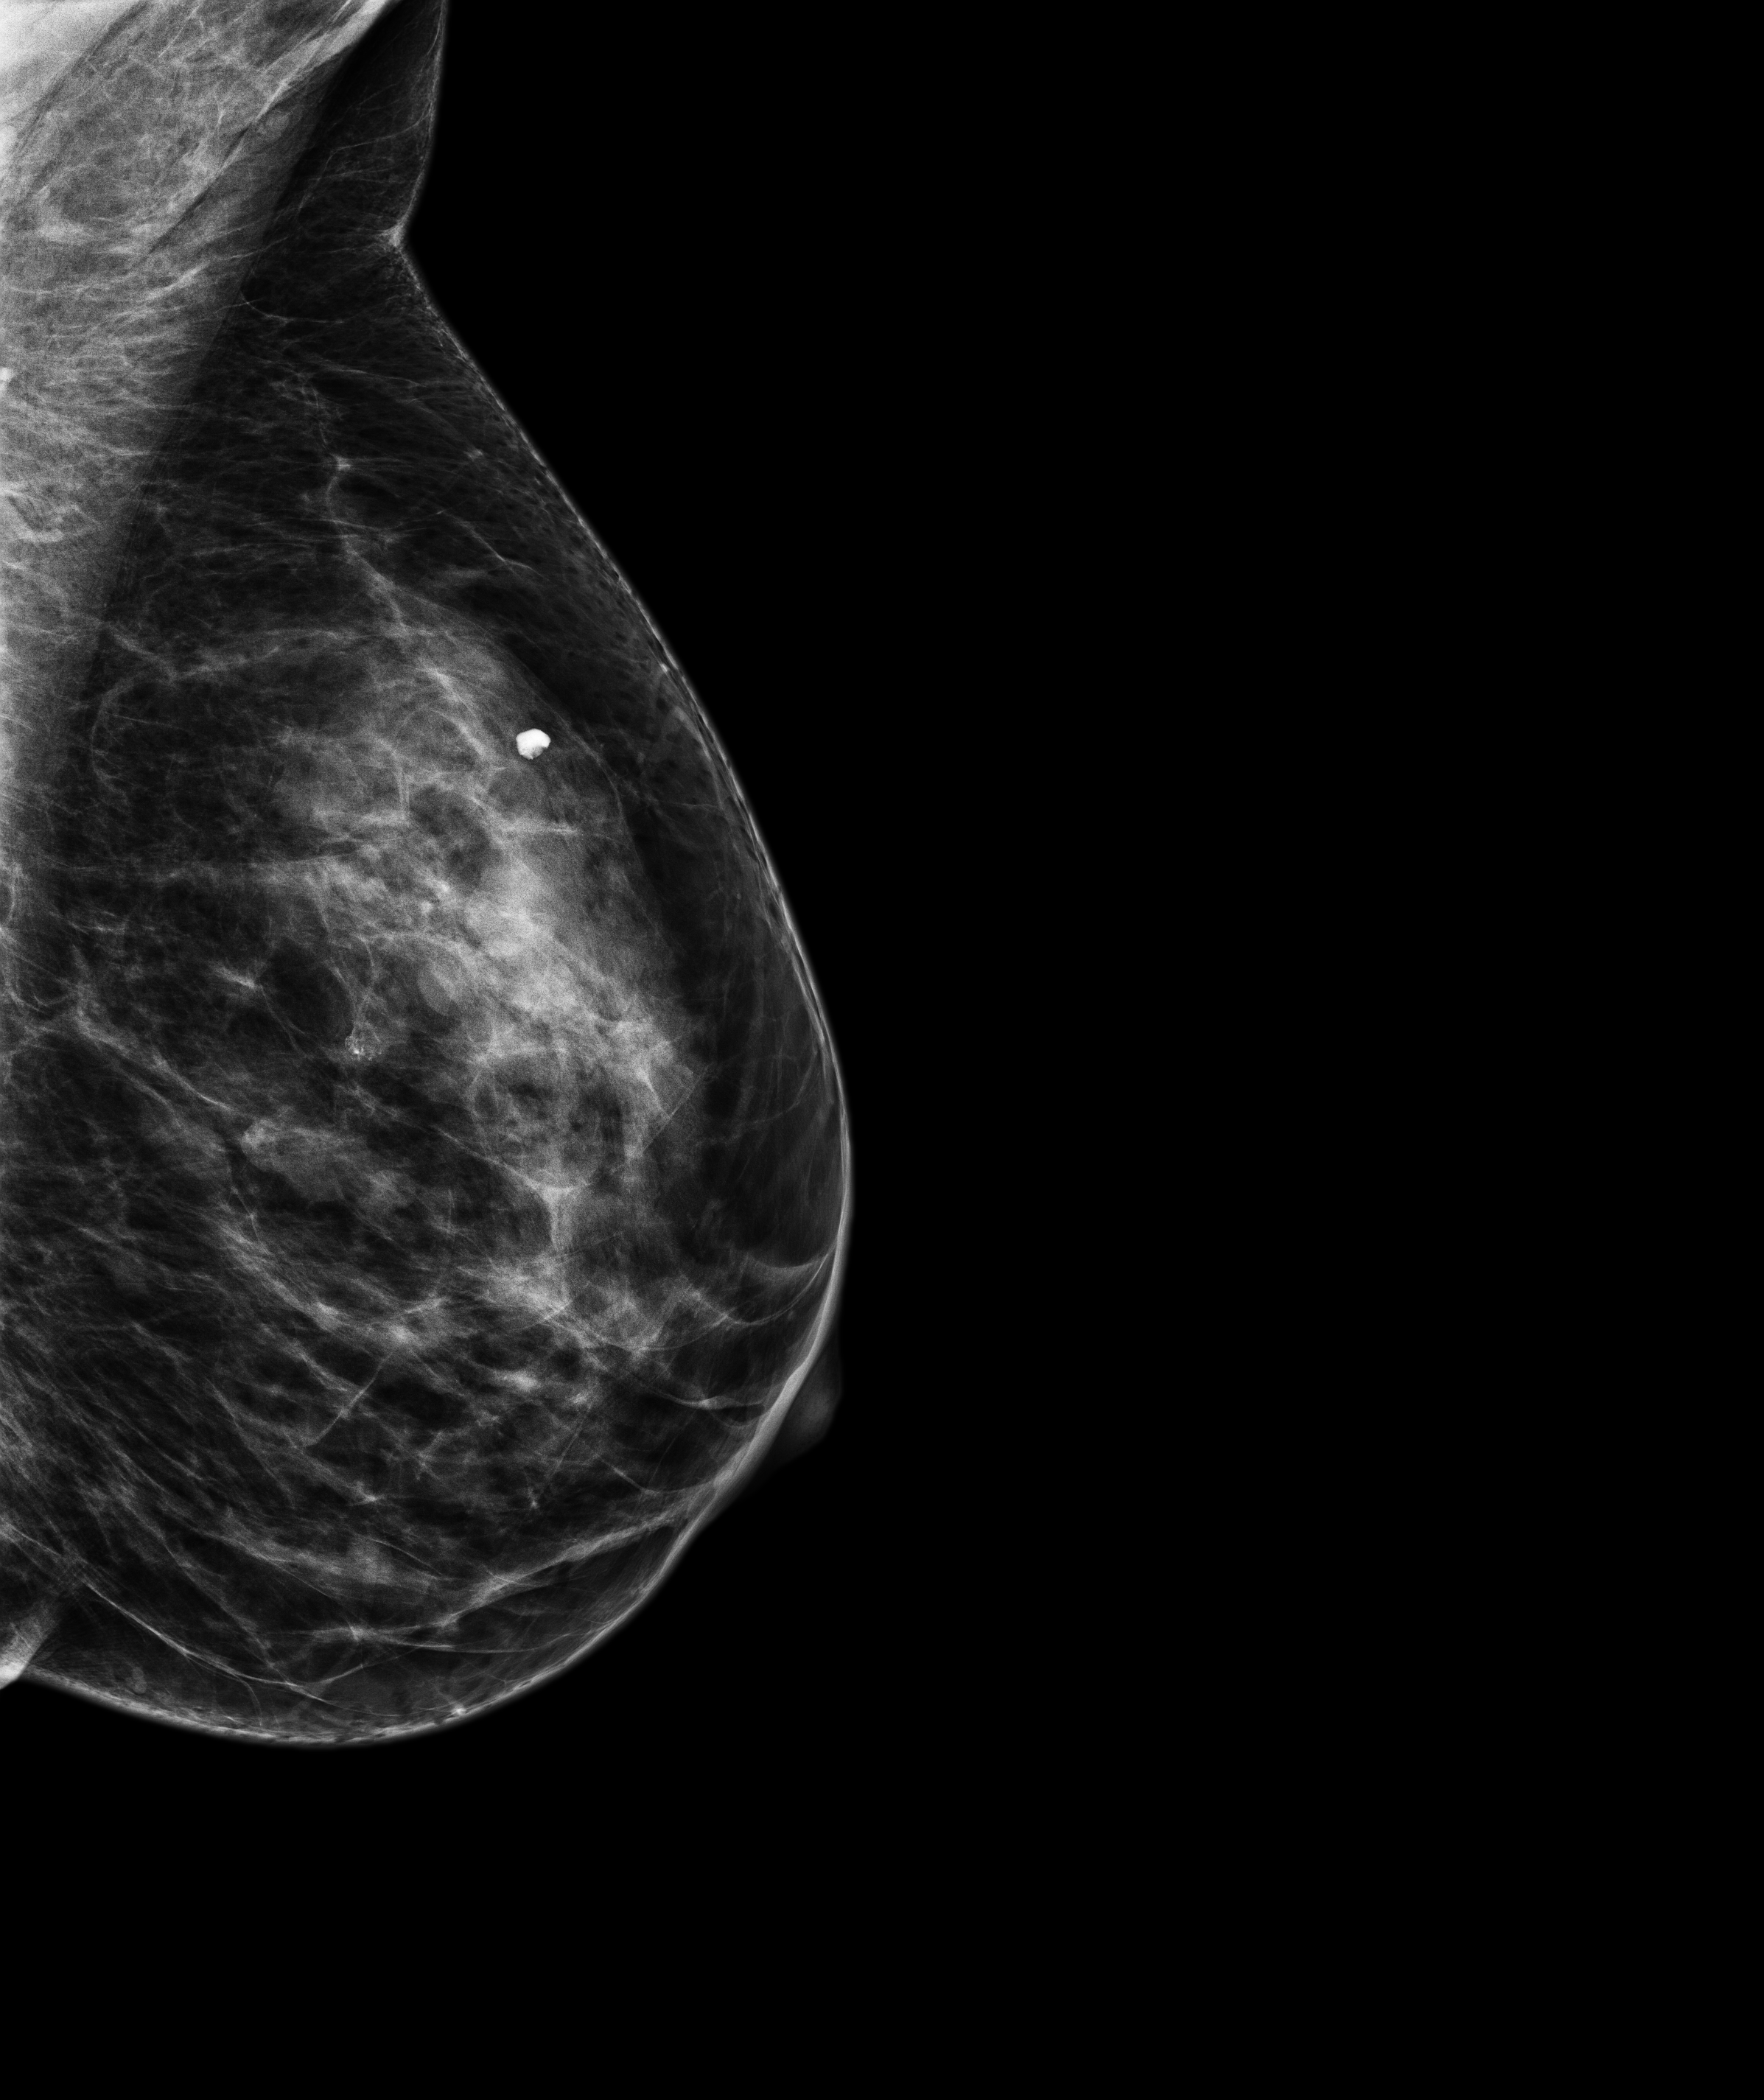
Screening examination, compressed breast thickness 60.3 mm. Patient aged 52 years (female).
Image type: full-field digital mammogram. Breast: left. Projection: medio-lateral oblique projection.